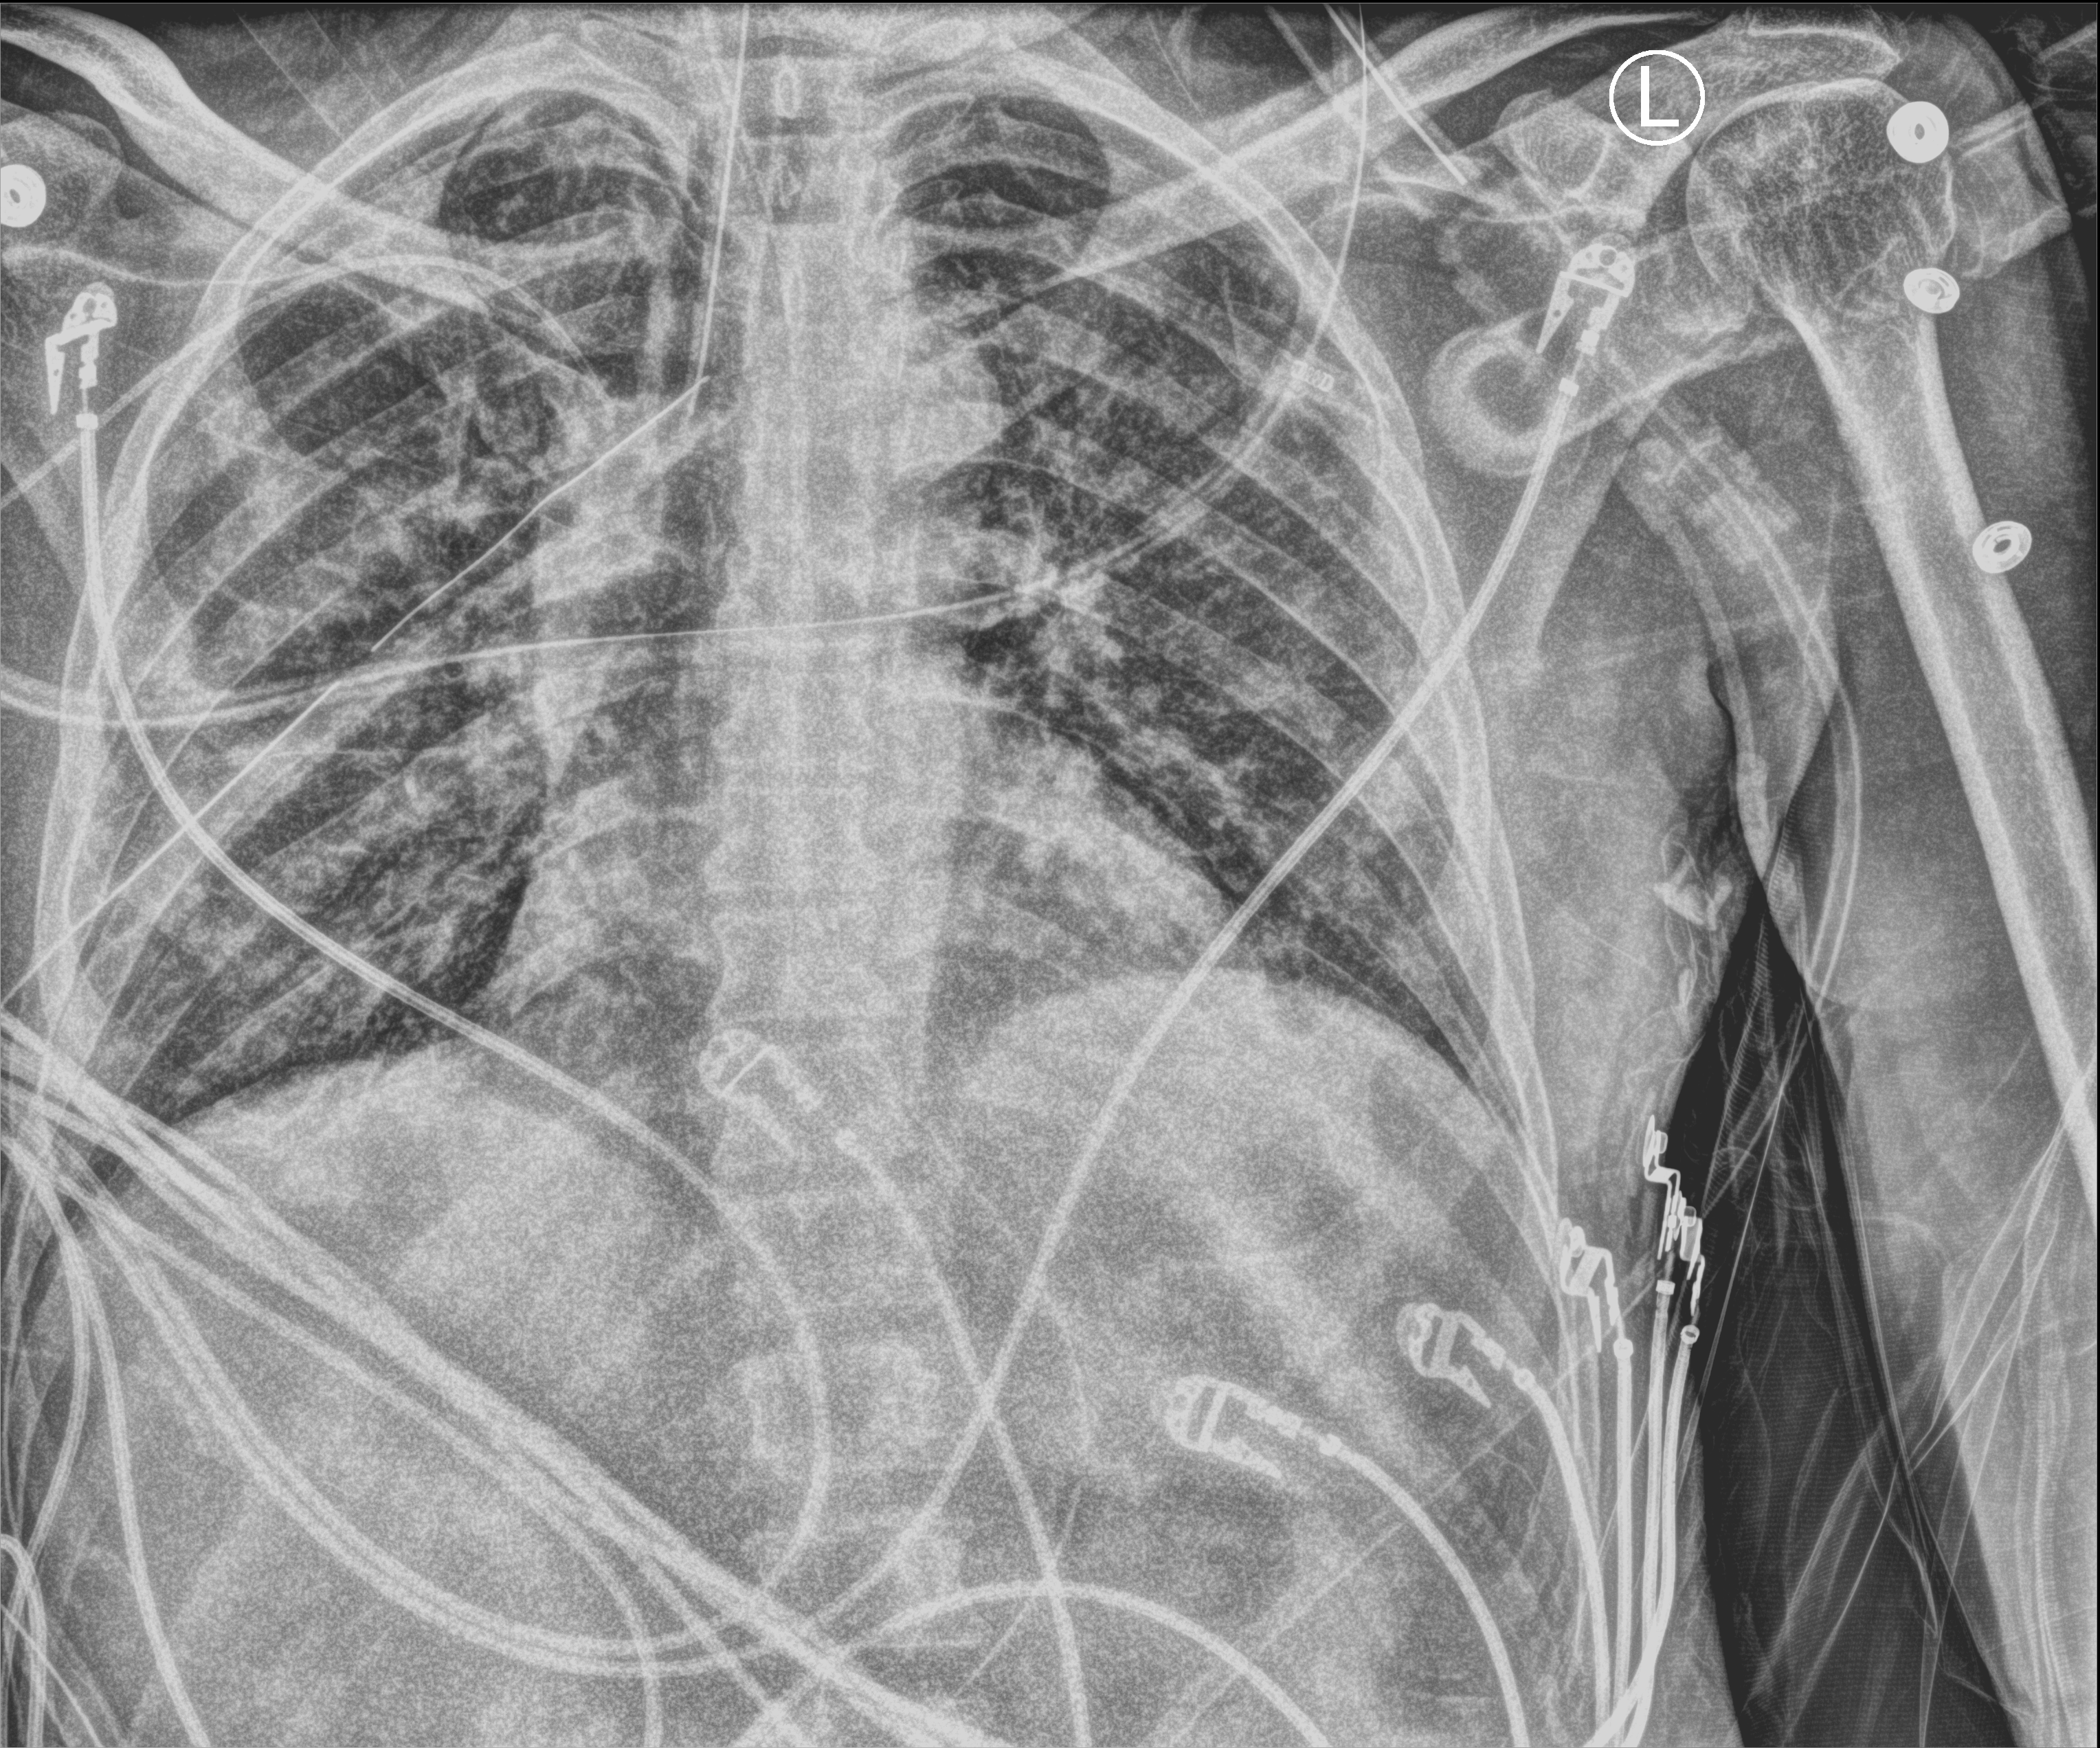
Chest X-ray (portable), anteroposterior (AP) projection. Patient hospitalised with COVID-19; male, aged 18–59 years.
From the hospital-stay record, not from the radiograph (when in the stay this image was taken is not recorded): mechanically ventilated during this hospital stay: yes; length of hospital stay: 41 days; diabetes (admission record): yes.